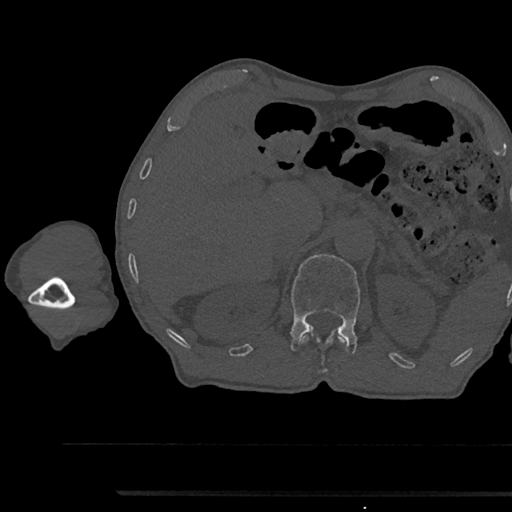
CT including the spine, one axial slice; slice 667 of 797 in the series (ordered by position); reconstruction kernel Br40s/3; 120 kVp; bone window (W 1800 / L 400 HU); 0.5 mm slice thickness; 512 × 512 image matrix. Male patient, age 79 years. Case-level facts recorded for this patient, not image findings: primary cancer: prostate.
Structures marked on this image (semi-automatic segmentation, software-assisted and operator-edited):
- L1 vertebra: bounding box (x1, y1, x2, y2) in pixels: (290, 254, 360, 354)
- T12 vertebra: (302, 333, 345, 344)